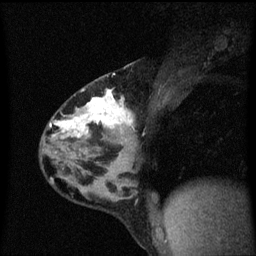
Breast MRI (dynamic contrast-enhanced), one sagittal slice. Slice 36 of 60 in the series (ordered by position). Dynamic contrast-enhanced series, image 2 of 3 at this slice position (ordered by acquisition). 1.5 T. TE 4.2 ms, TR 8.4 ms. 2 mm slice thickness. 256 × 256 image matrix, field of view 200 × 200 mm. Patient: female, 32 years.
Annotated regions visible in this slice (semi-automatically segmented with operator editing):
- analysis volume of interest (the breast-tissue region the enhancement analysis was run in; not a lesion): box from (x=40, y=74) to (x=139, y=169) px
- tumour enhancement mask (voxels above the 70 % enhancement threshold inside the analysis volume of interest): (x=50, y=90)–(x=134, y=155)